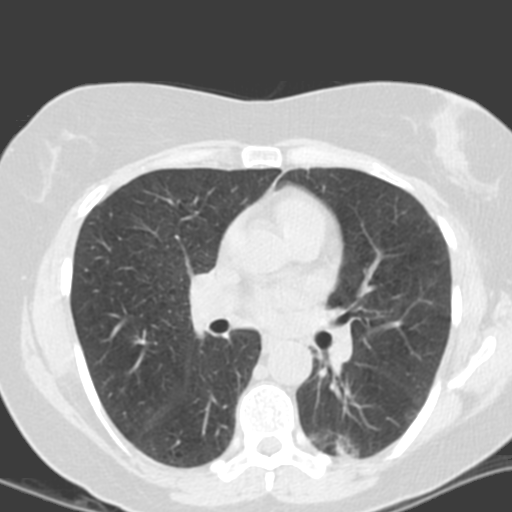
Axial slice from a low-dose chest CT screening exam, second annual screen, lung window (W 1500 / L -600 HU), 3.2 mm slice thickness. Female participant, aged 55 years at enrolment. Current smoker at enrolment.
Expert reader's lesion annotation, bounding box <304,410,380,471> (left, top, right, bottom; pixels). The screening reader recorded 4 non-calcified nodules or masses ≥4 mm on this exam (left lower lobe, left lower lobe, left upper lobe, right middle lobe); which of them this box marks is not recorded. Official screen result: positive, other. Lung cancer was diagnosed 688 days after this screen (after the third annual screen): adenocarcinoma with mixed subtypes, left lower lobe, poorly differentiated (G3), stage IA (AJCC 6th edition), 21 mm at pathology.